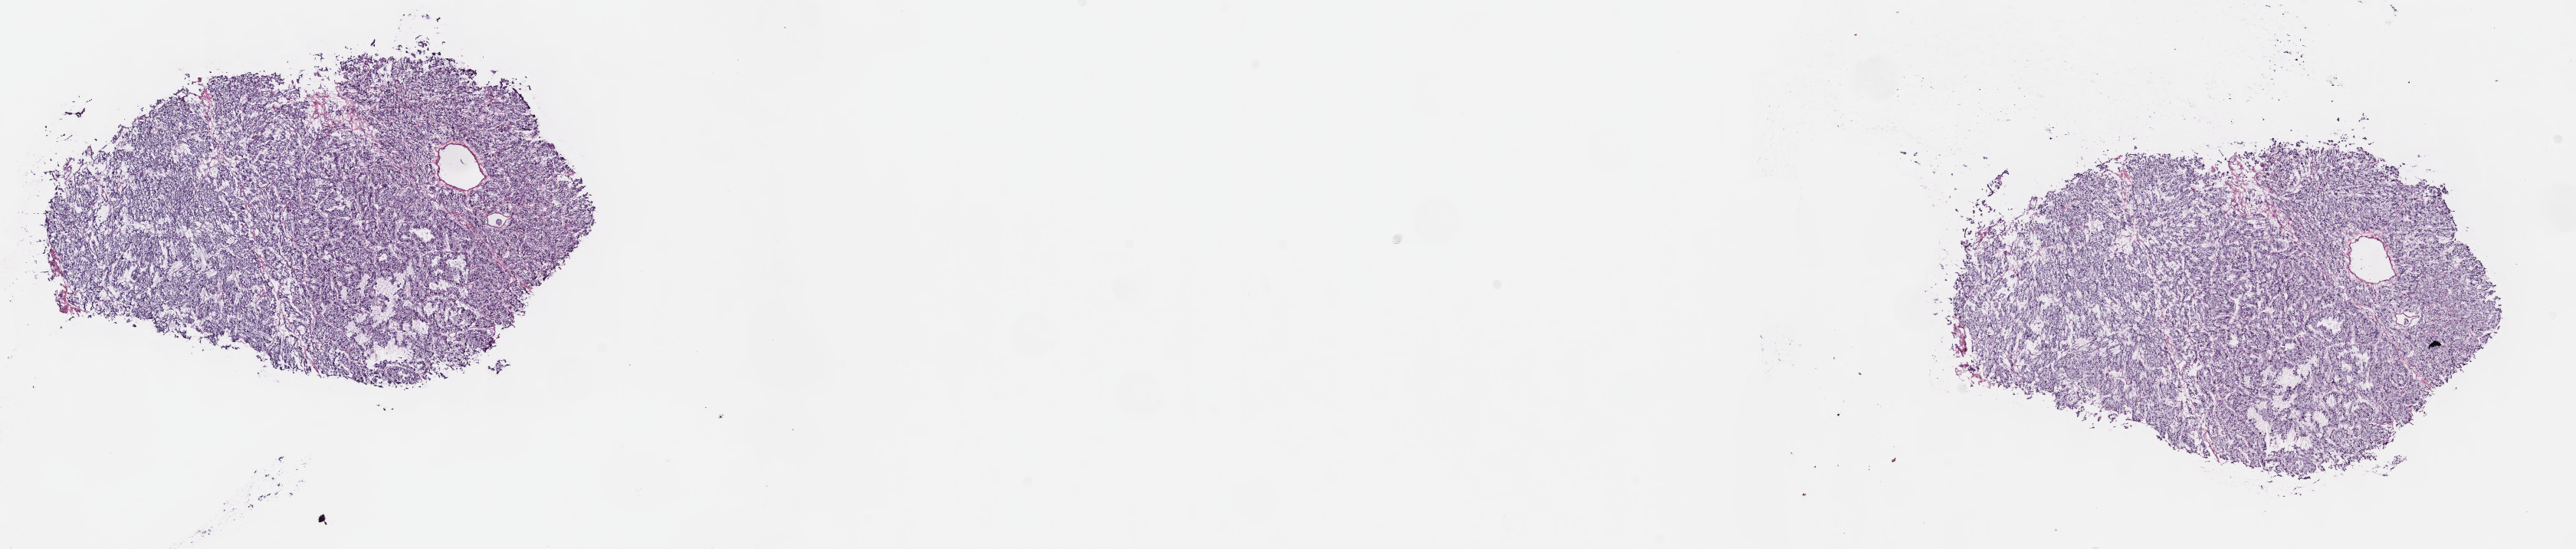
Digitized H&E tissue section (whole slide) — low-resolution overview of the scanned area, about 27.2 x 5.8 mm (slide scanned at 40x), frozen section from the top of the tissue portion, primary tumour sample from the adrenal gland. Male, age 36 years at initial diagnosis. Composition of this section per pathologist review: tumour cells 85%, tumour nuclei 85%.
Histologic diagnosis: Pheochromocytoma, malignant.